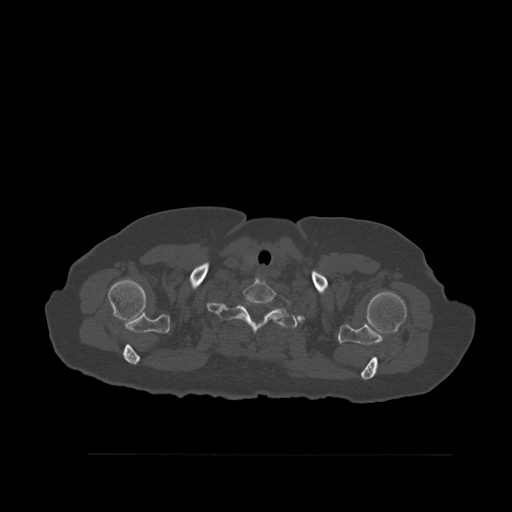
CT including the spine, one axial slice. Position 447 of 527 along the scan axis. Bone window (W 1800 / L 400 HU). 512 × 512 image matrix, field of view 470 × 470 mm. Female patient, age 73 years. From the clinical record (not read from this slice): primary cancer: breast.
Annotated regions visible in this slice (semi-automatic segmentation, software-assisted and operator-edited):
- T1 vertebra: bounding box <216,301,298,335> (left, top, right, bottom; pixels)